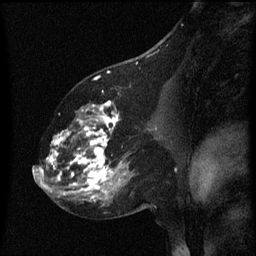
Breast MRI (dynamic contrast-enhanced), one sagittal slice; position 32 of 60 along the scan axis; dynamic contrast-enhanced series, image 2 of 3 at this slice position (ordered by acquisition); 1.5 T; TE 4.2 ms, TR 8 ms; 256 × 256 image matrix, field of view 200 × 200 mm. Patient: female, 60 years.
Annotated regions visible in this slice (semi-automatically segmented with operator editing):
- analysis volume of interest (the breast-tissue region the enhancement analysis was run in; not a lesion): box from (x=49, y=102) to (x=158, y=197) px
- tumour enhancement mask (voxels above the 70 % enhancement threshold inside the analysis volume of interest): (x=49, y=102)–(x=120, y=197)